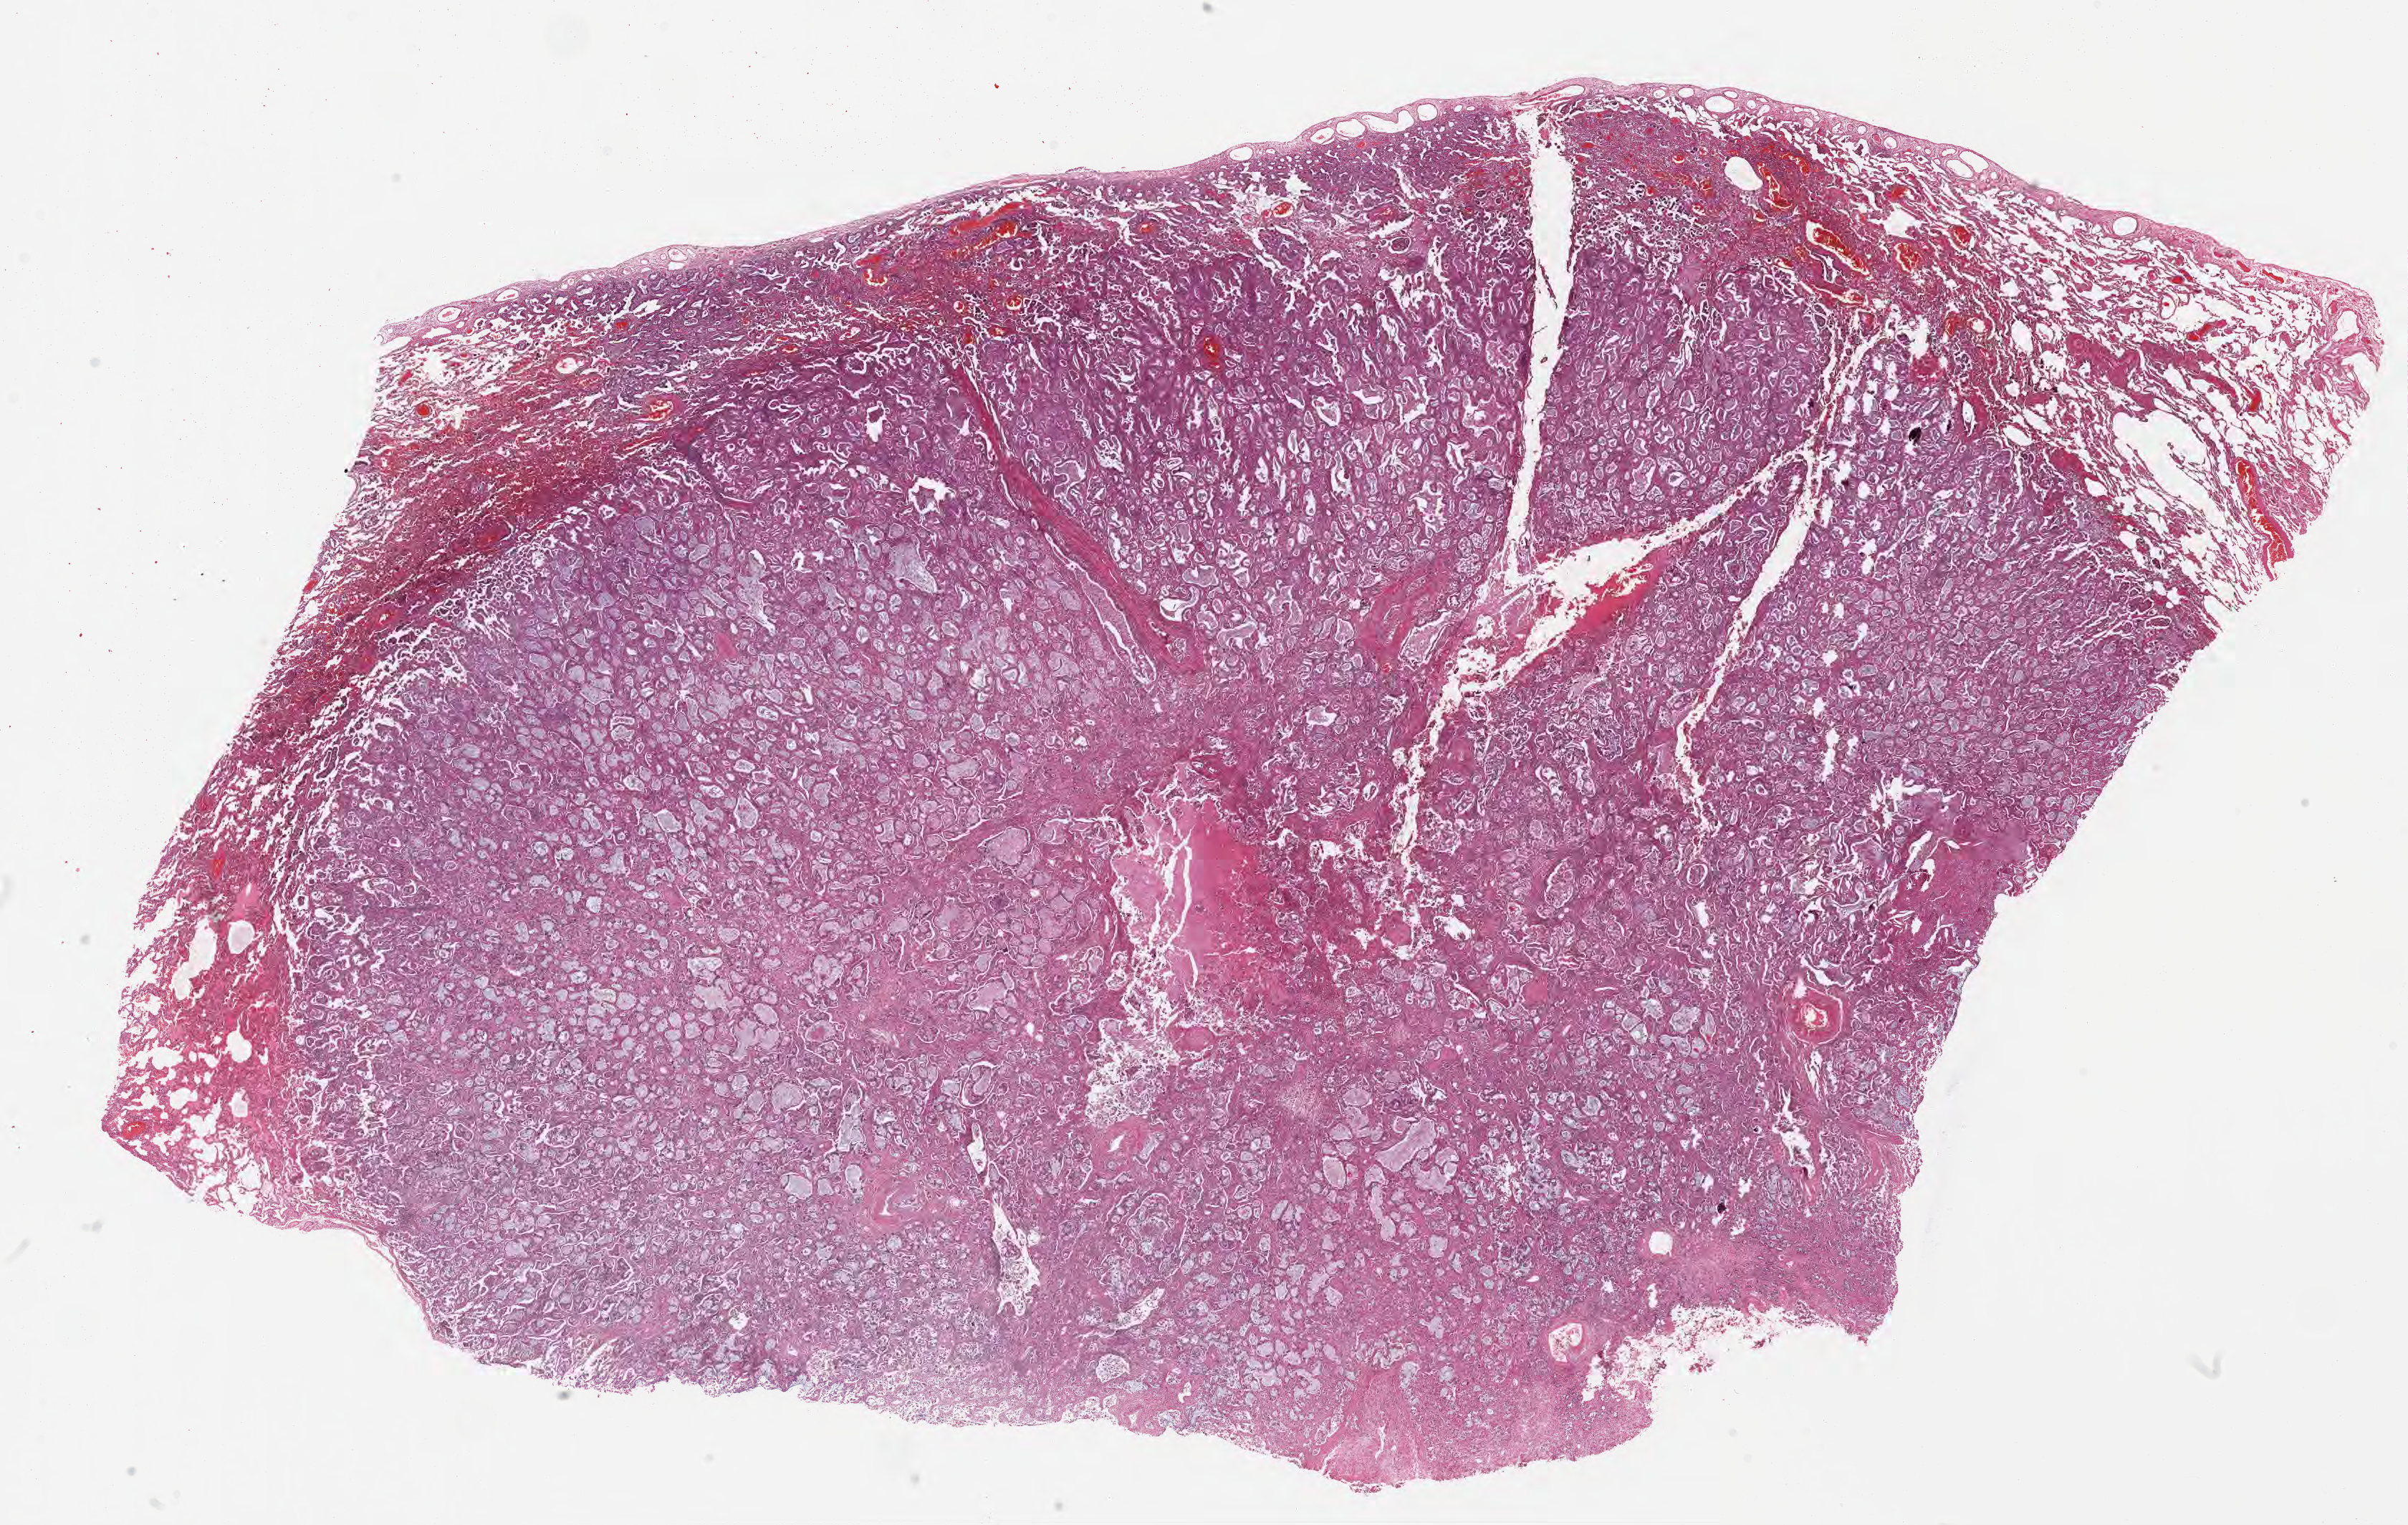
Digitized haematoxylin and eosin-stained section, shown as a low-resolution overview of the whole scanned area (about 27.2 x 17.2 mm). Formalin-fixed paraffin-embedded section. Primary tumor. Site: lower lobe of right lung. Patient: female, 71 years old. Slide review estimates, as recorded: tumor cells 88%, tumor nuclei 75%, stromal cells 0%, necrosis 0%, normal cells 12%. Inflammatory infiltration, as recorded: lymphocyte infiltration 0%, monocyte infiltration 0%, neutrophil infiltration 0%.
AJCC pathologic stage: Stage IIA. Histologic diagnosis: Acinar cell carcinoma.